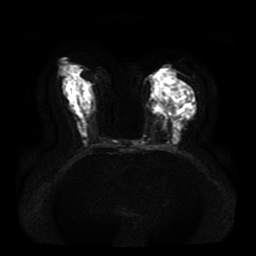
Breast MRI, one axial slice. Diffusion-weighted series; image 2 of 4 stored at this slice position (different b-values; order by instance number). 1.5 T. 5 mm slice thickness. 256 × 256 image matrix, field of view 330 × 330 mm. Female patient.
Outlined on this slice (expert manual segmentation):
- tumour on diffusion-weighted imaging: bounding box (x1, y1, x2, y2) in pixels: (179, 102, 186, 105)